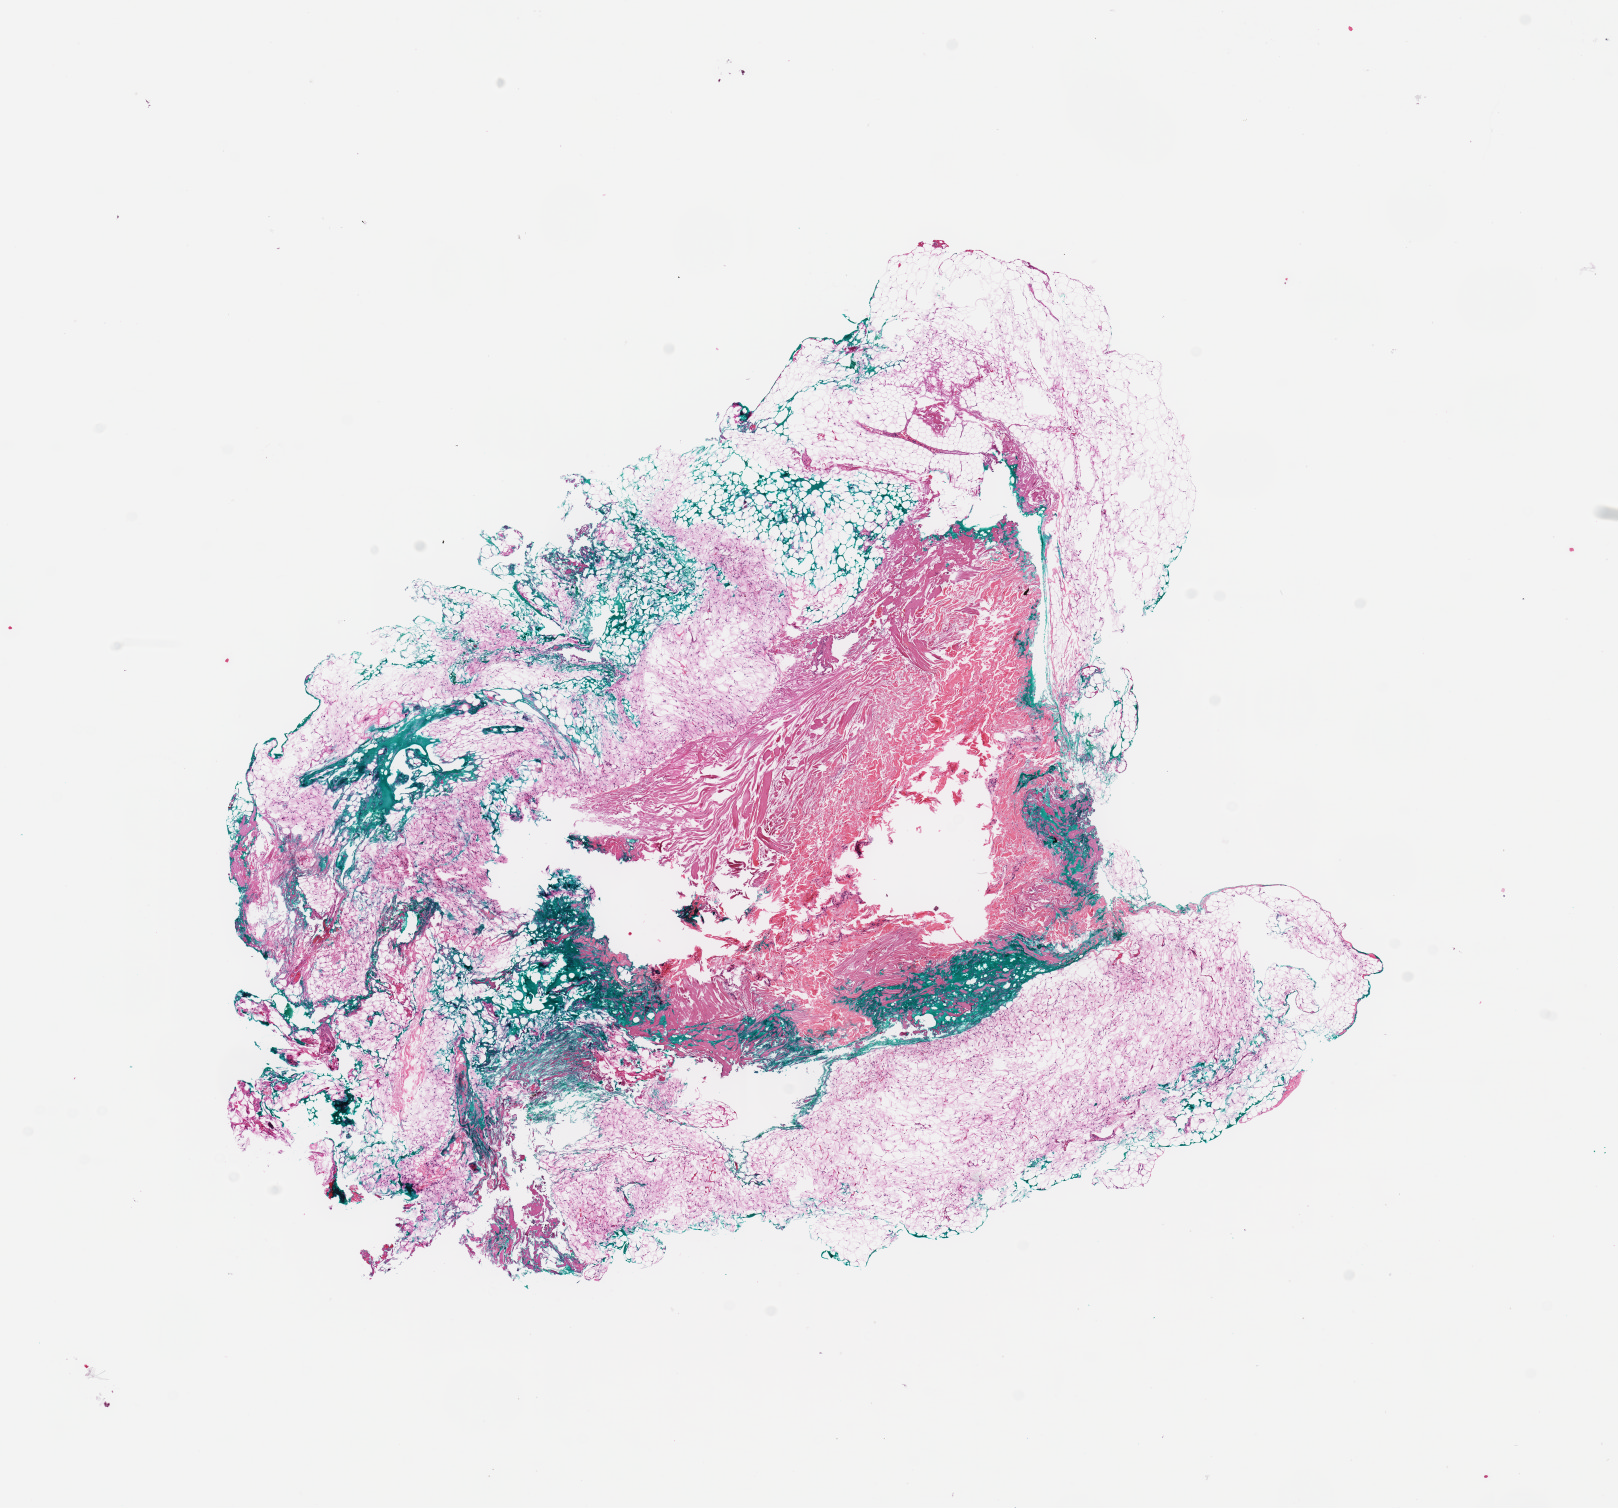
Hematoxylin and eosin (H&E) stained whole-slide image — whole scanned area (about 12.8 x 11.9 mm, from a 20x scan) shown as a low-resolution overview. Normal (non-tumour) tissue sample, sampled site: trunk. 83-year-old male patient.
This section: normal (non-tumour) tissue from the same patient. Patient diagnosis: Malignant melanoma, NOS.